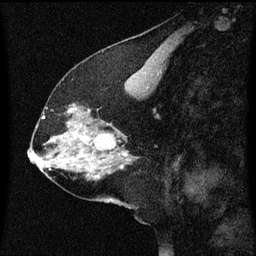
Breast MRI (dynamic contrast-enhanced), one sagittal slice. Position 27 of 60 along the scan axis. Dynamic contrast-enhanced series, image 2 of 3 at this slice position (ordered by acquisition). 1.5 T. TE 4.2 ms, TR 8 ms. 256 × 256 image matrix. Female patient, age 58 years.
Structures marked on this image (semi-automatic segmentation, software-assisted and operator-edited):
- analysis volume of interest (the breast-tissue region the enhancement analysis was run in; not a lesion): bounding box <56,104,95,137> (left, top, right, bottom; pixels)
- tumour enhancement mask (voxels above the 70 % enhancement threshold inside the analysis volume of interest): <70,108,77,135>